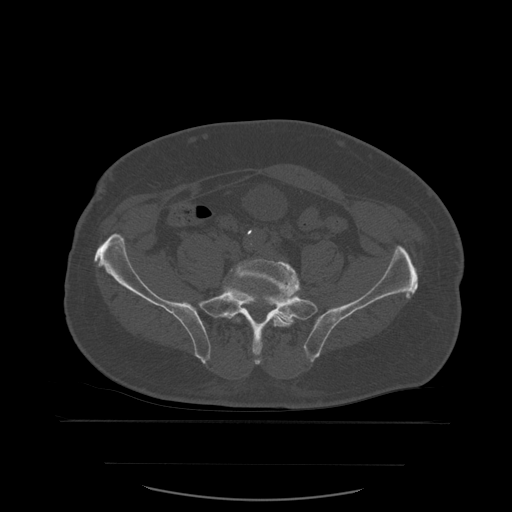
CT including the spine, one axial slice. Position 125 of 590 along the scan axis. Bone window (W 1800 / L 400 HU). 1.25 mm slice thickness. 512 × 512 image matrix, field of view 479 × 479 mm. Patient age 71 years. Case-level facts recorded for this patient, not image findings: primary cancer: lung.
Outlined on this slice (semi-automatic segmentation, software-assisted and operator-edited):
- L5 vertebra: bounding box (x1, y1, x2, y2) in pixels: (219, 259, 300, 356)